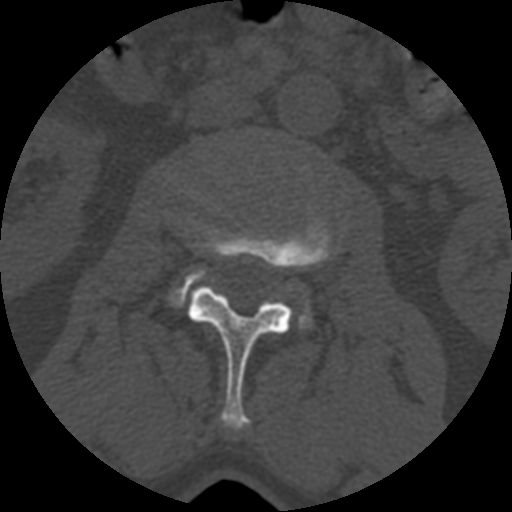
CT including the spine, one axial slice; position 326 of 399 along the scan axis; reconstruction kernel STANDARD; bone window (W 1800 / L 400 HU); 512 × 512 image matrix. Patient age 71 years. Case-level facts recorded for this patient, not image findings: primary cancer: prostate.
Annotated regions visible in this slice (semi-automatic segmentation, software-assisted and operator-edited):
- L2 vertebra: box from (x=185, y=220) to (x=333, y=431) px
- L3 vertebra: (x=167, y=269)–(x=312, y=330)